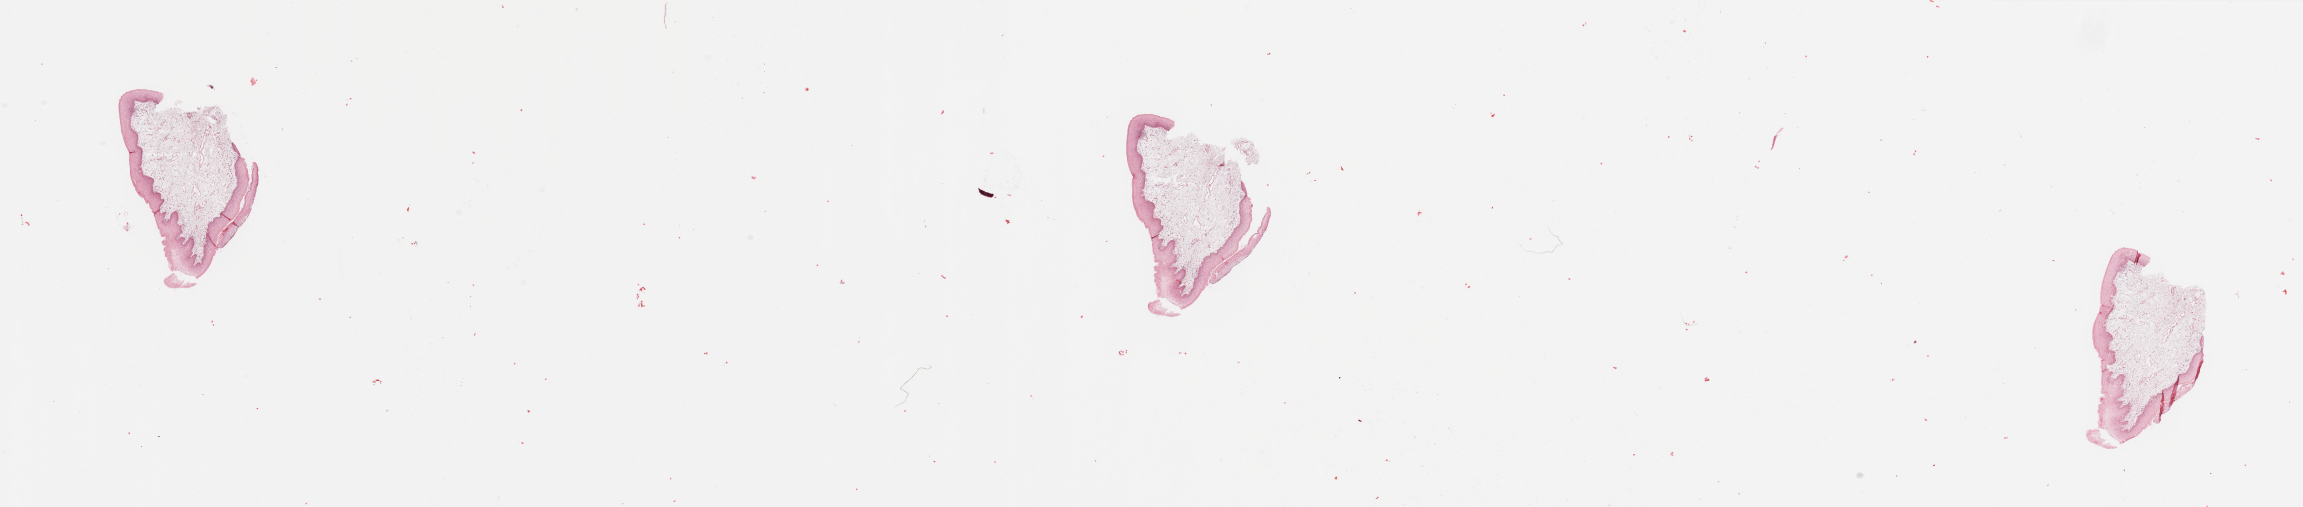
Whole-slide histology image, Hematoxylin and eosin (H&E) stained — whole scanned area (about 36.4 x 8.0 mm, from a 20x scan) shown as a low-resolution overview; head and neck, tissue type not recorded. 58-year-old male patient.
Patient diagnosis: Squamous cell carcinoma, NOS (floor of mouth, NOS).